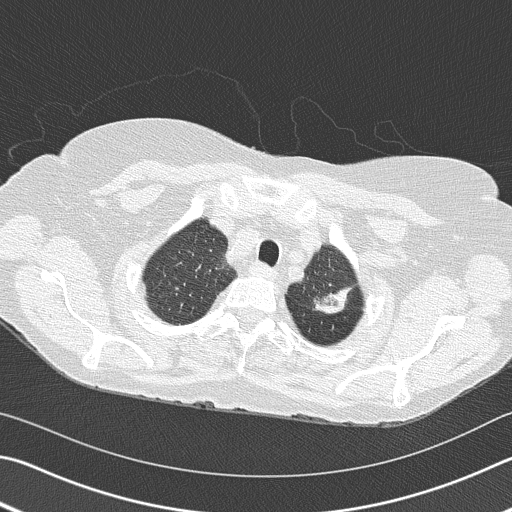
Low-dose screening chest CT, axial slice. Second screening round (one year after baseline). Lung window (W 1500 / L -600 HU). 2 mm slice thickness. Slice 135 of 153 in the series. Female, age 68 years at enrolment. Former smoker at enrolment.
- Expert reader's lesion annotation, bounding box (x1, y1, x2, y2) in pixels: (289, 248, 368, 330).
- The exam's reader record, not a measurement of the box and not confirmed to be the same lesion: non-calcified nodule or mass ≥4 mm, left upper lobe, 4 × 2 mm, spiculated (stellate) margins, soft tissue attenuation, pre-existing on the prior screen: yes; interval growth: yes.
- Official screen result: positive, other.
- Lung cancer was diagnosed 392 days after this screen (after the third annual screen): adenocarcinoma, NOS, left upper lobe, poorly differentiated (G3), stage IB (AJCC 6th edition), 50 mm at pathology.